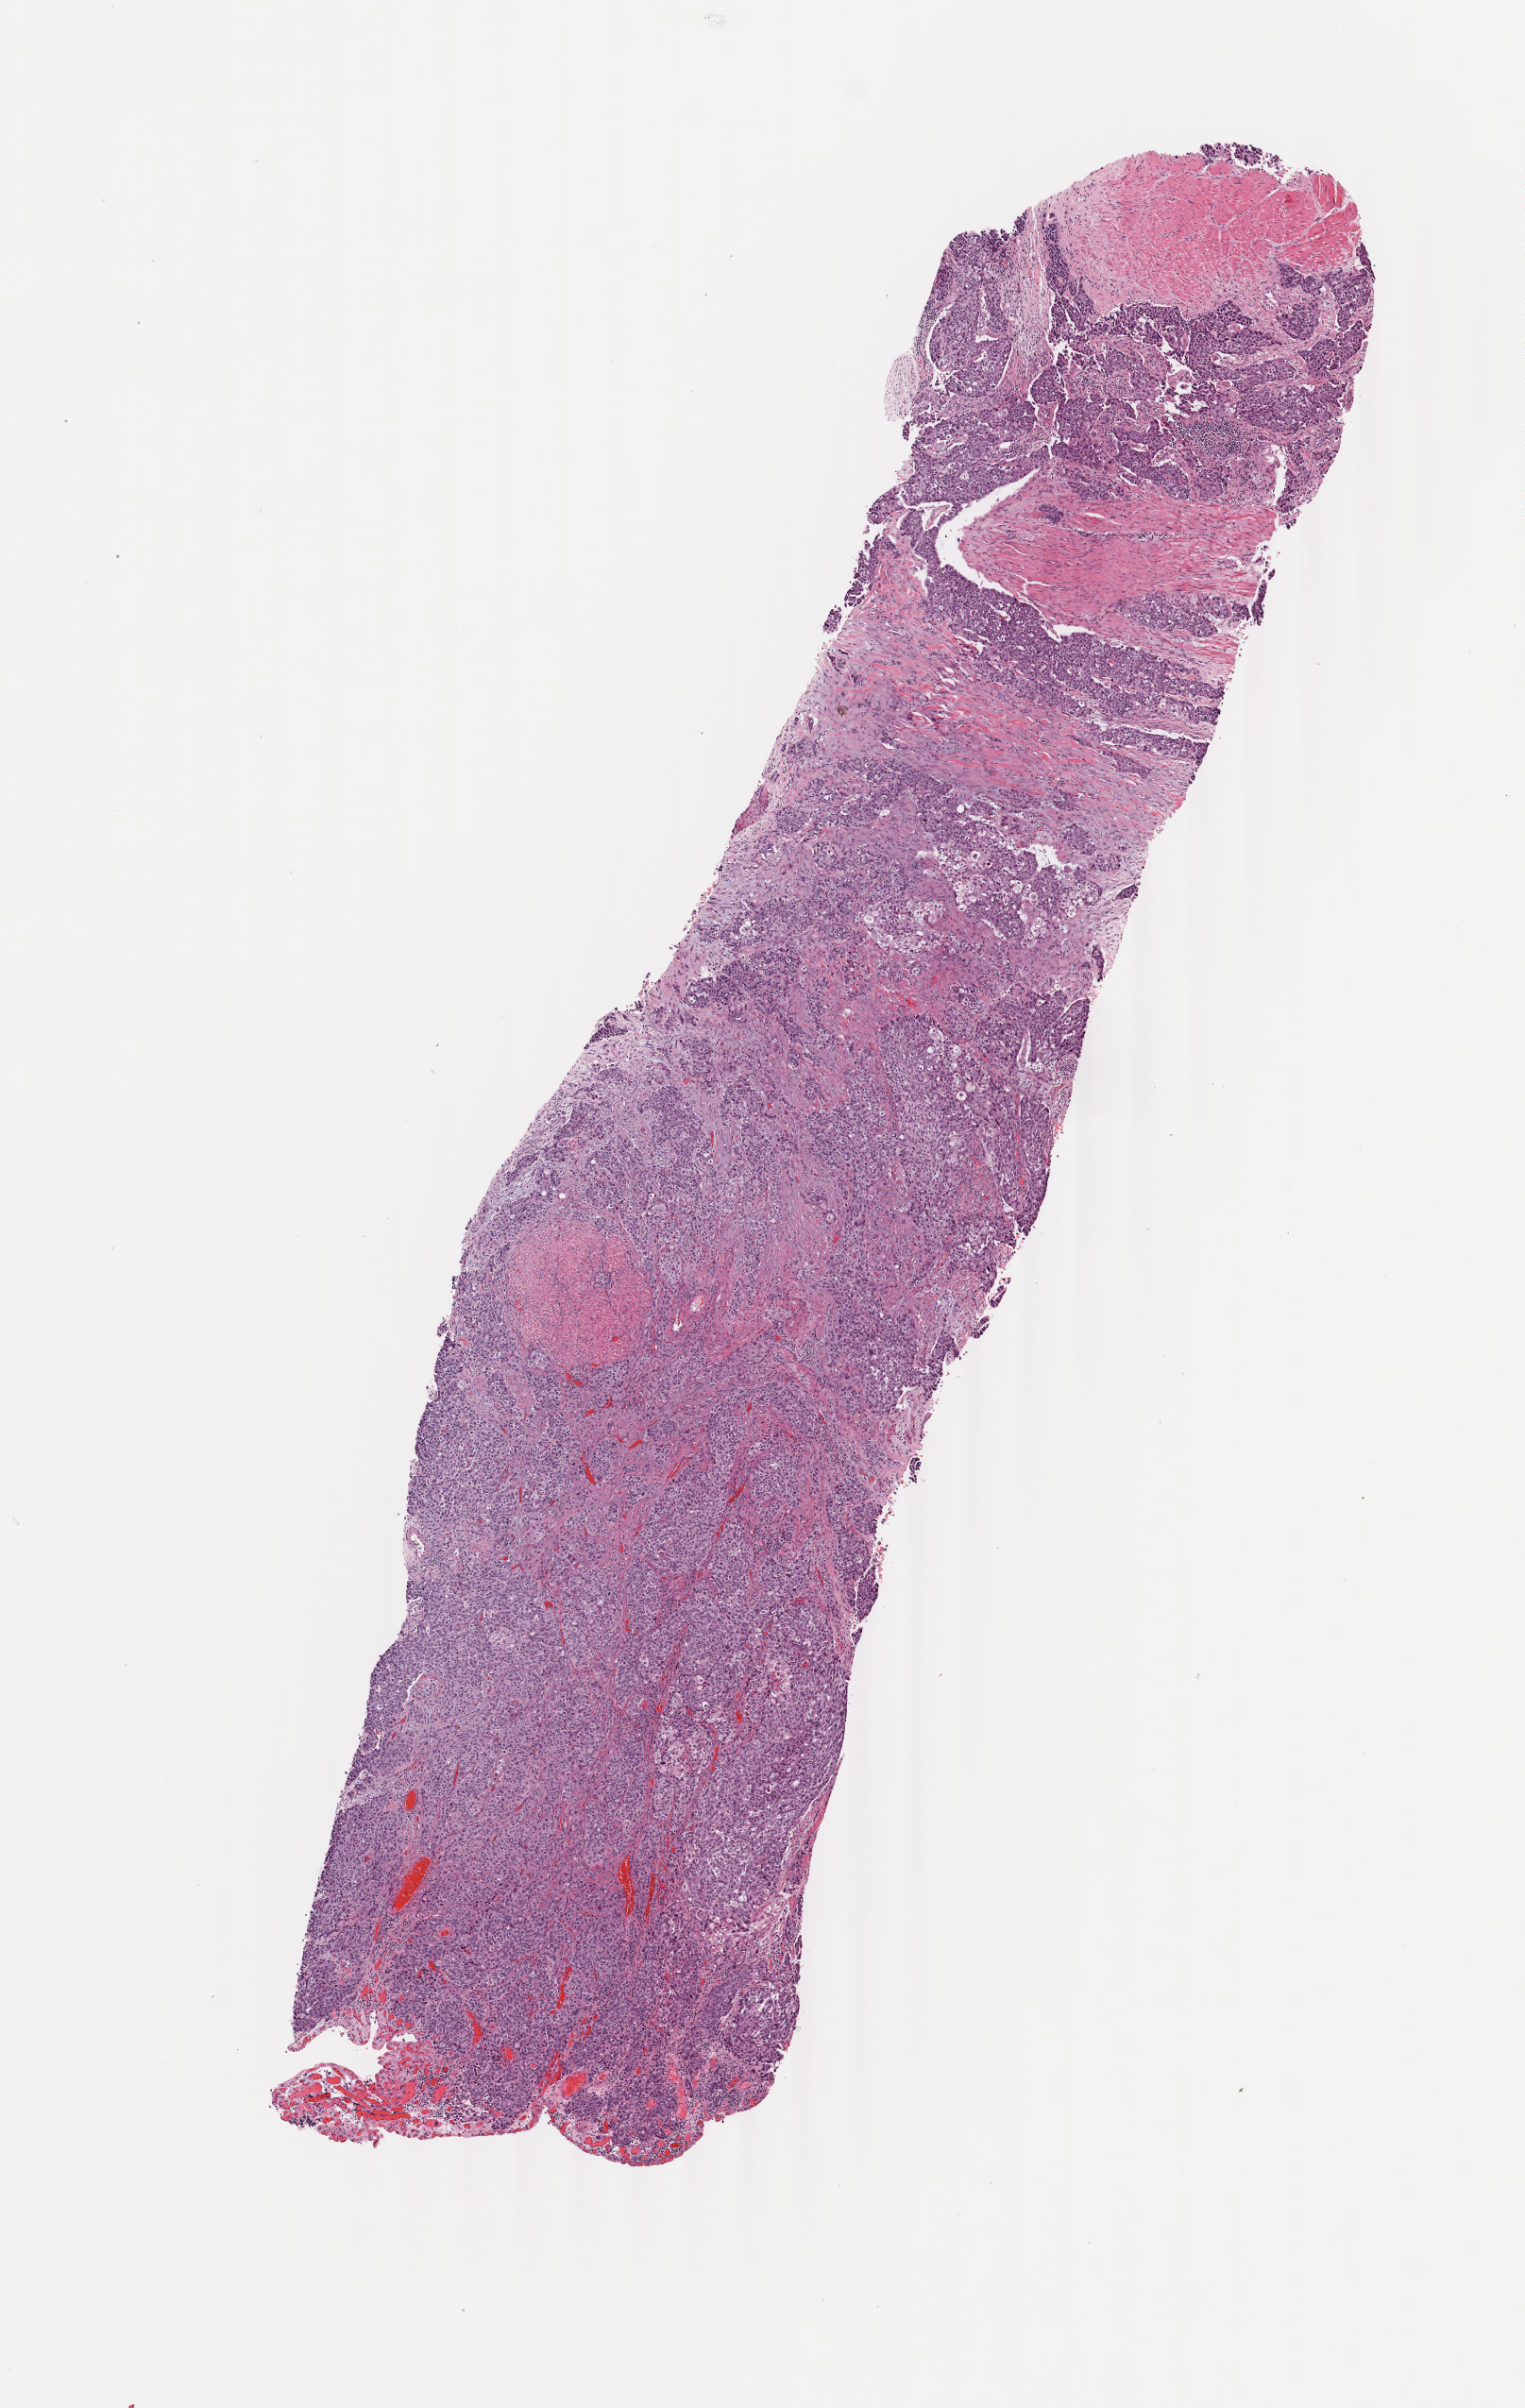
Whole-slide histology image, H&E, low-resolution overview of the scanned area, about 6.4 x 10.1 mm (acquisition: 40x scan), frozen section from the bottom of the tissue portion, primary tumour sample from the bladder. Male patient; age at initial diagnosis 65 years. Histologic grade: high grade. Pathologist review of this section (percent, as recorded): tumour cells 80%, tumour nuclei 80%, normal cells 15%, stromal cells 5%, necrosis 0%. Infiltration values recorded for this section: lymphocyte infiltration 0%, monocyte infiltration 0%, neutrophil infiltration 0%.
* AJCC pathologic stage: IV
* histologic diagnosis: Transitional cell carcinoma
* TNM: T4 N2 M0
* lymph nodes positive (case pathology): 2 of 11 examined